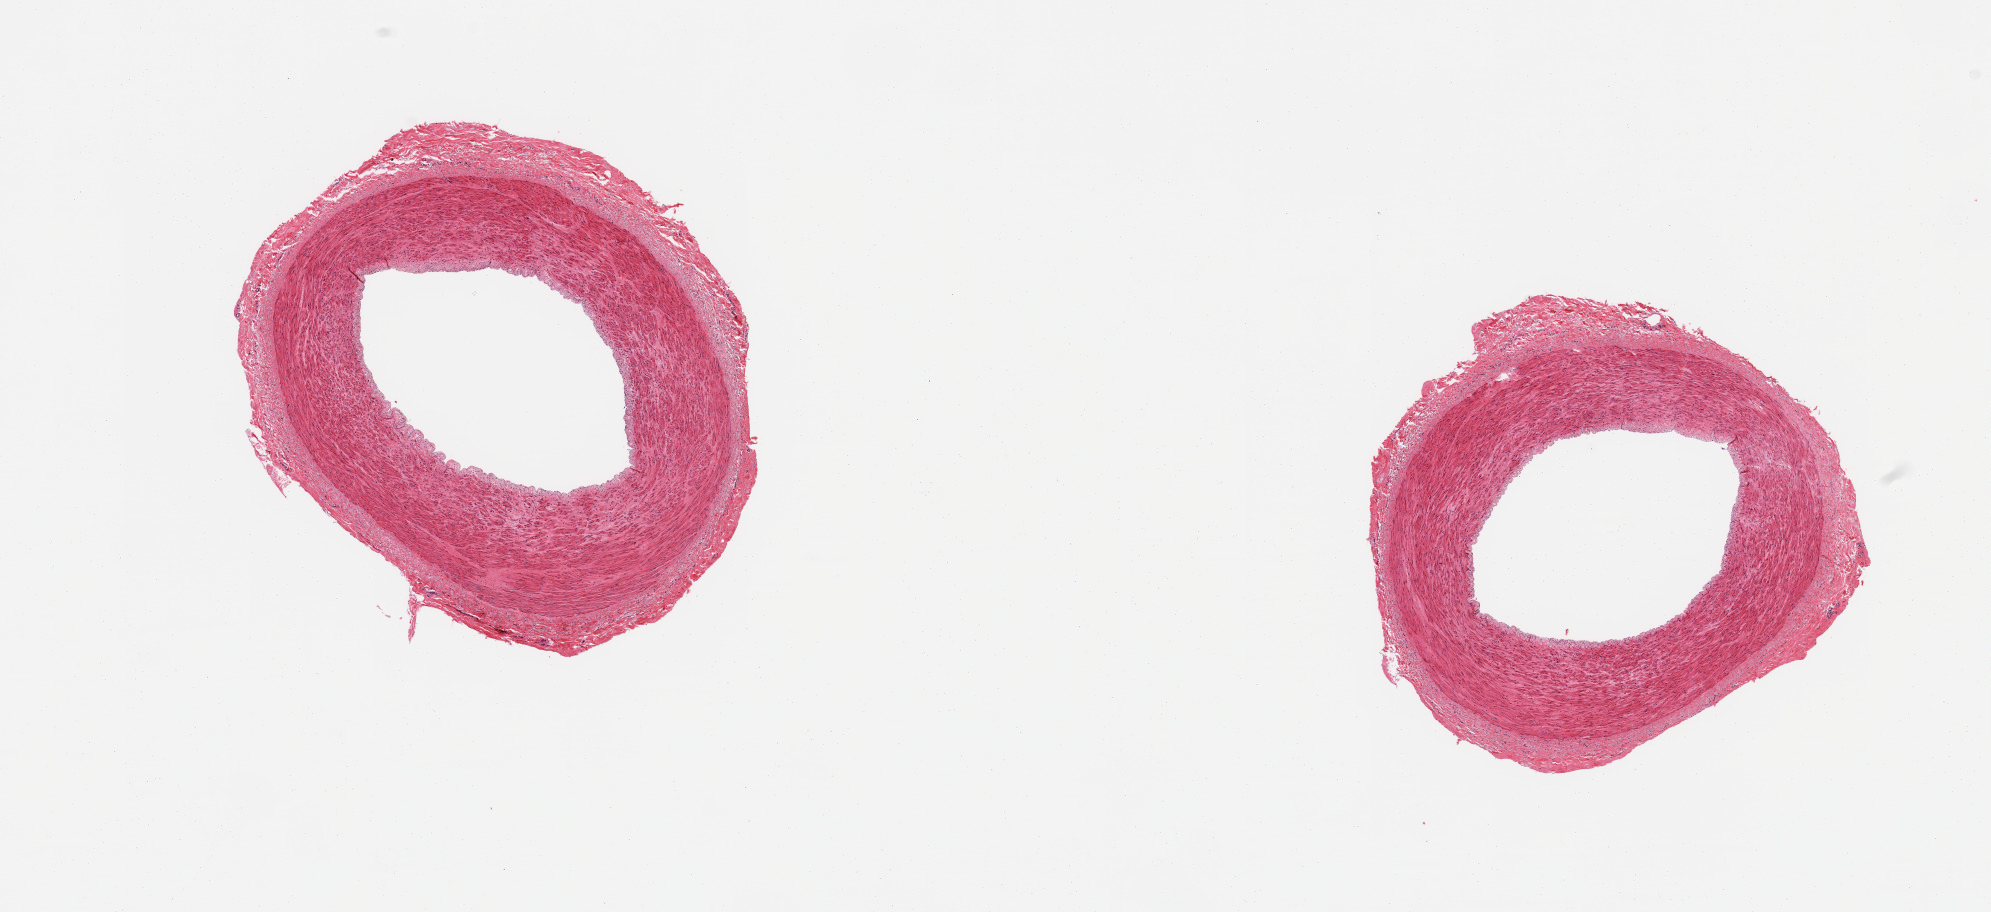
H&E whole-slide image — shown as a low-resolution overview of the whole scanned area (about 15.8 x 7.2 mm, from a 20x scan), PAXgene-fixed, paraffin-embedded tissue, target tissue: tibial artery, donor tissue sample. Donor sex: male.
Review note (as recorded): 2 pieces; well trimmed, no lesions.